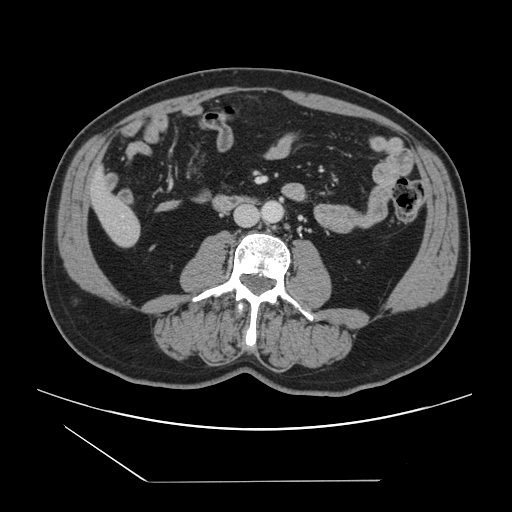
Contrast-enhanced abdominal CT, one axial slice; slice 19 of 157 in the series (ordered by position); 120 kVp; intravenous contrast given; soft-tissue window (W 400 / L 40 HU); 2.5 mm slice thickness; 512 × 512 image matrix, field of view 407 × 407 mm. Male patient, age 61 years. Case-level facts recorded for this patient, not image findings: diagnosis: colorectal cancer liver metastases, imaged before liver resection; multiple liver metastases: yes; largest metastasis: 5.5 cm; disease in both lobes: yes.
Structures marked on this image (manually delineated by an expert):
- liver: bounding box <92,174,140,246> (left, top, right, bottom; pixels)
- planned liver remnant (the part of the liver to remain after resection): <92,173,126,218>